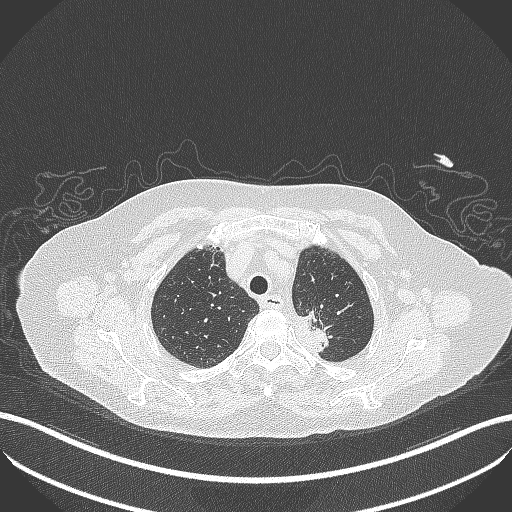
Chest CT, one axial slice. Slice 282 of 353 in the series (ordered by position). Reconstruction kernel B70f. Lung window (W 1500 / L -600 HU). 1 mm slice thickness. 512 × 512 image matrix. Patient: female, 81 years. From the clinical record (not read from this slice): clinical TNM (as recorded): T2a N0 M0.
Structures marked on this image (rectangle marked by the reading radiologist):
- lung tumour (recorded histology: adenocarcinoma): bounding box [x1, y1, x2, y2] px = [282, 300, 335, 356]